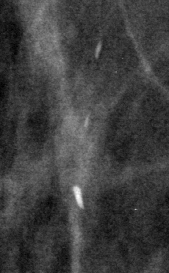
Cropped region of a digitized screen-film mammogram centred on a radiologist-marked abnormality; right breast; MLO view; BI-RADS breast density category 1 (scale 1–4).
Calcifications, distribution regional; BI-RADS assessment category 2; benign without callback (not worked up further).